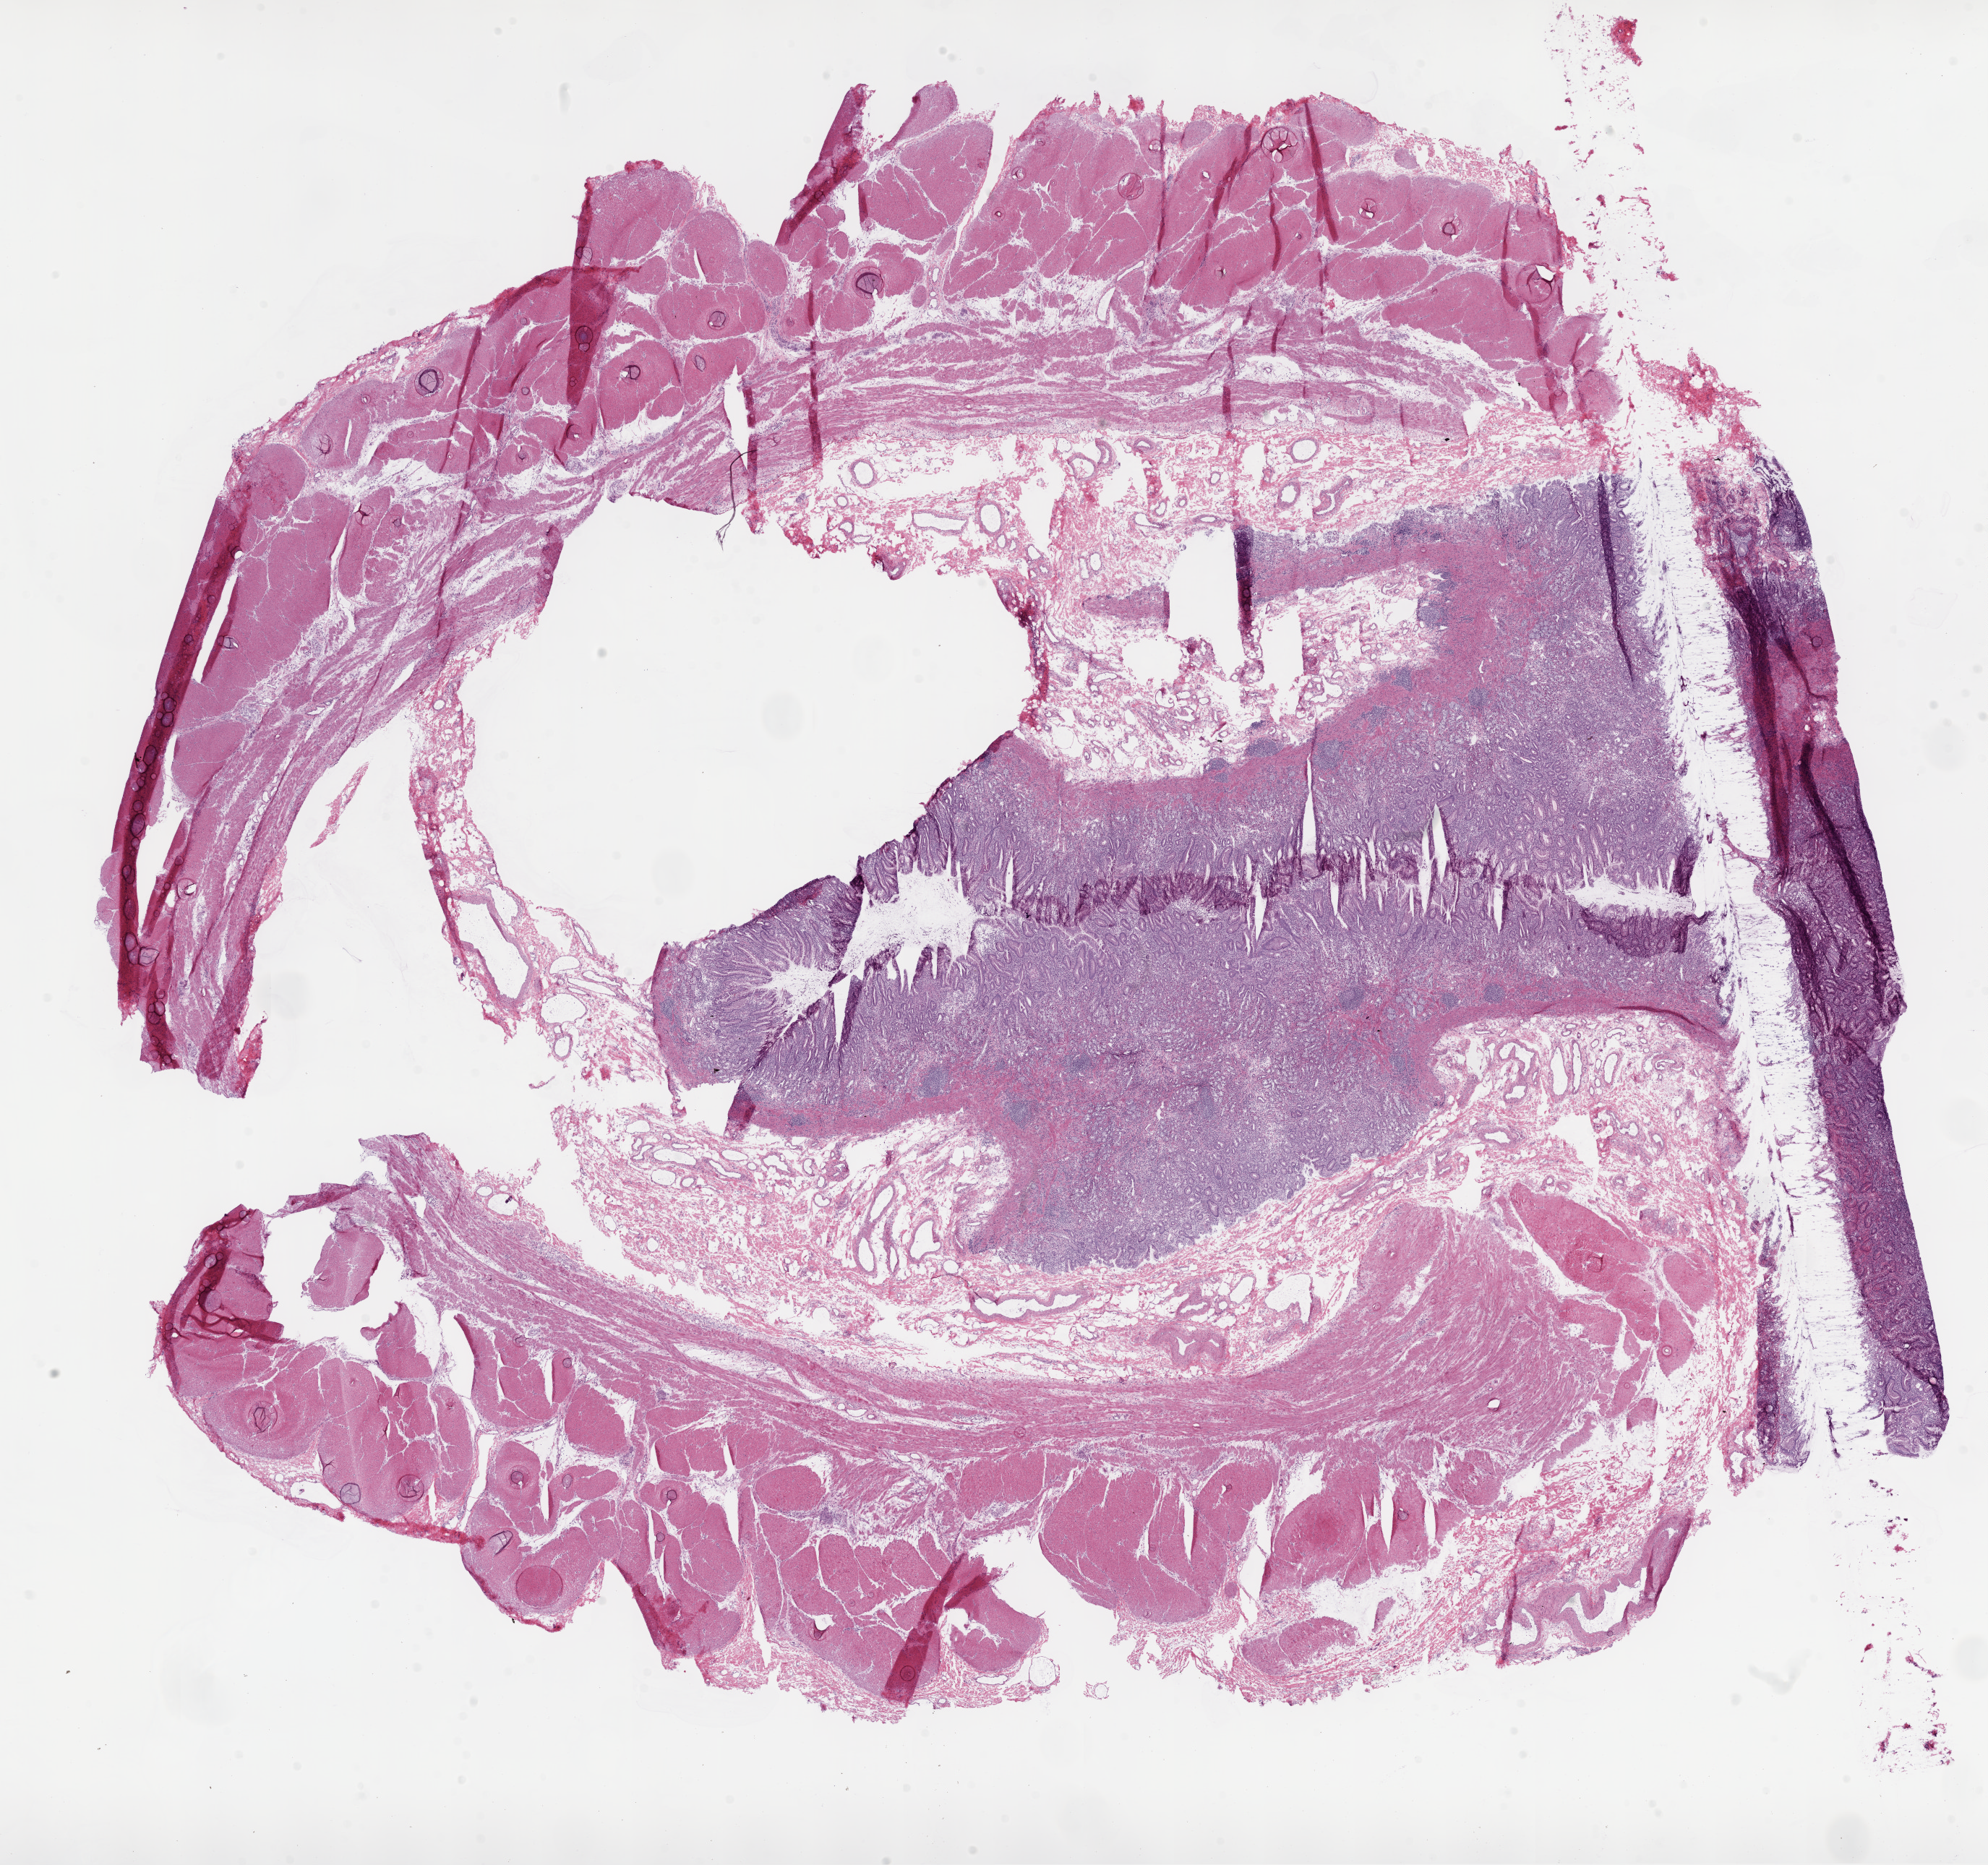
H&E whole-slide image — low-resolution overview of the scanned area, about 22.1 x 20.7 mm (from a 20x scan); frozen section from the bottom of the tissue portion; sample: solid tissue normal (non-tumour tissue), stomach. Female patient; age at initial diagnosis 78 years.
* this section: solid tissue normal sample (biorepository sample class)
* patient diagnosis: Adenocarcinoma, NOS (gastric antrum)